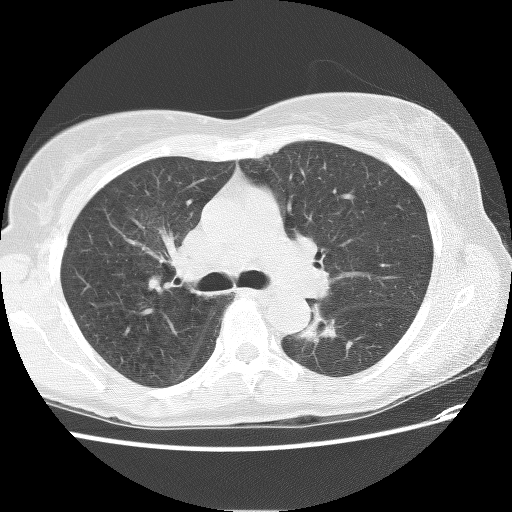
Low-dose screening chest CT, axial slice; baseline screening round; lung window (W 1500 / L -600 HU); 2.5 mm slice thickness; lung (sharp) reconstruction kernel (BONE). Female participant, aged 62 years at enrolment. Former smoker at enrolment.
• Lesion marked by an expert reader, bounding box (x1, y1, x2, y2) in pixels: (290, 303, 342, 344).
• No non-calcified nodule or mass ≥4 mm was recorded by the screening reader at this exam.
• Official screen result: negative screen, minor abnormalities not suspicious for lung cancer.
• Participant outcome: lung cancer diagnosed 898 days after this screen — squamous cell carcinoma, NOS, left lower lobe, stage IIIB (AJCC 6th edition), 31 mm at pathology.